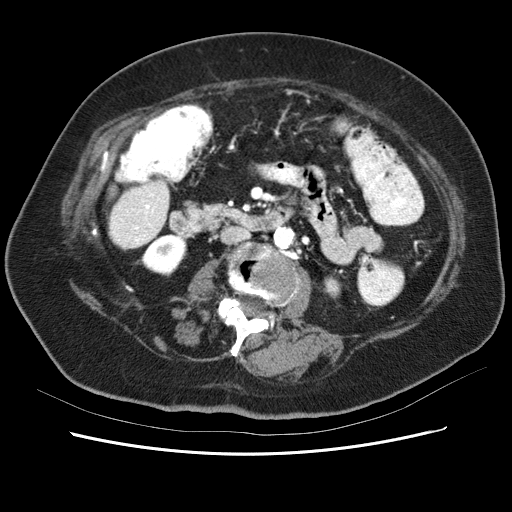
Contrast-enhanced abdominal CT (liver protocol), one axial slice; slice 10 of 62 in the series (ordered by position); reconstruction kernel STANDARD; soft-tissue window (W 400 / L 40 HU); 512 × 512 image matrix, field of view 340 × 340 mm. Case-level facts recorded for this patient, not image findings: diagnosis: hepatocellular carcinoma (patient treated with transarterial chemoembolisation; whether this scan precedes or follows treatment is not stated here); TNM stage (as recorded): Stage-I; Child-Pugh class: B; tumour nodularity: uninodular; tumour size: 5.3 cm.
Annotated regions visible in this slice (semi-automatic segmentation, software-assisted and operator-edited):
- liver parenchyma outside the tumour (the mass and vessels are separate outlines, so this box may not span the whole liver): bounding box <104,178,170,253> (left, top, right, bottom; pixels)
- liver vessels: <110,185,164,239>